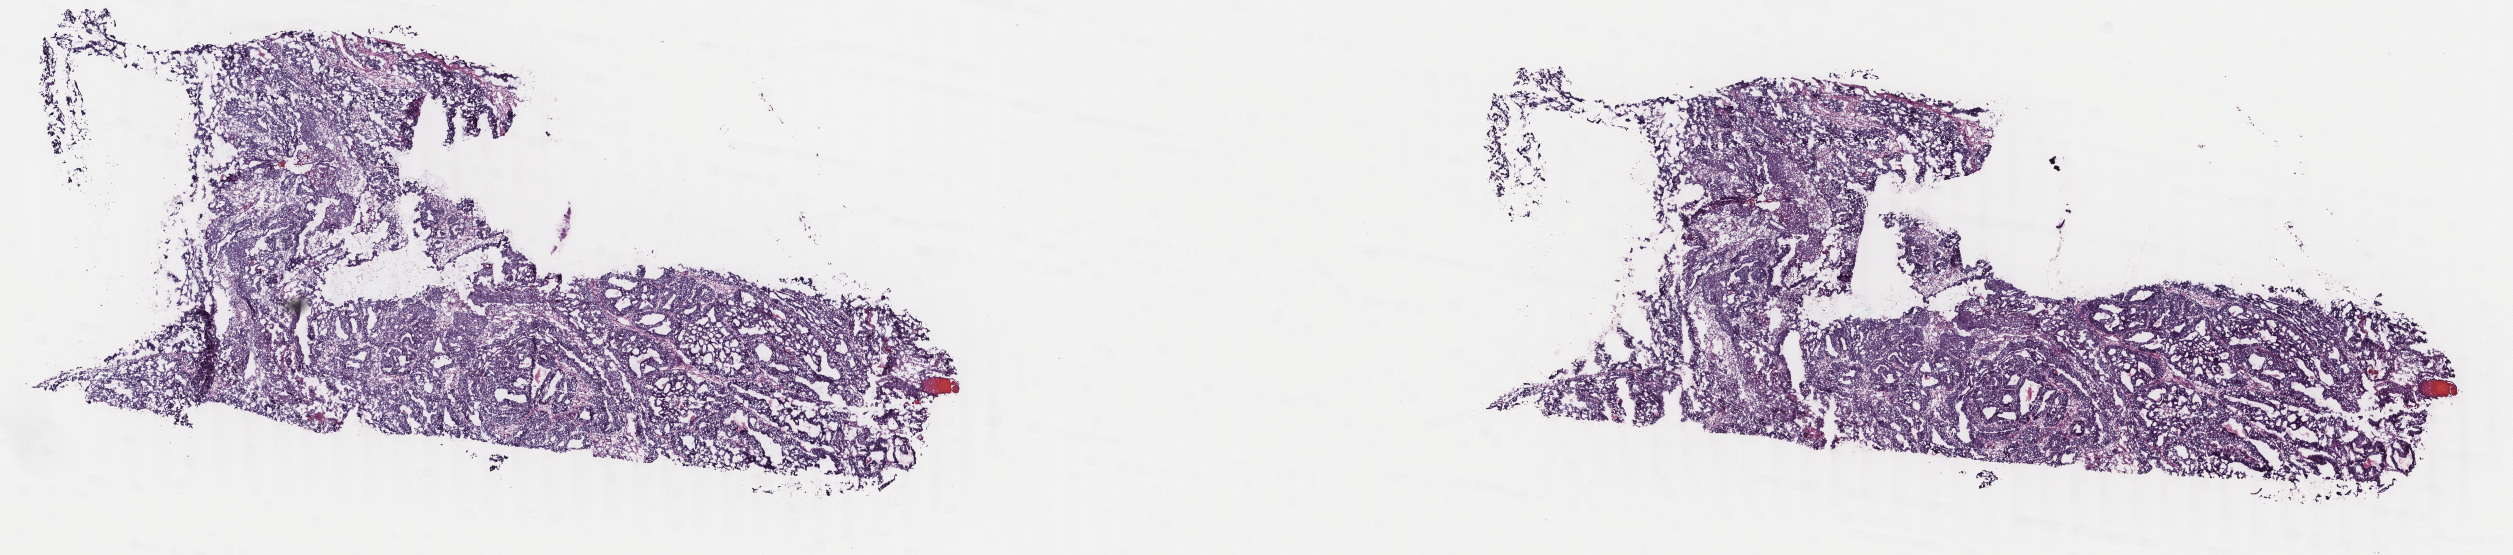
H&E whole-slide image, shown as a low-resolution overview of the whole scanned area (about 20.0 x 4.4 mm, from a 40x scan), frozen section, uterus, primary tumour sample. Patient: female, age at initial diagnosis 55 years. Histologic grade: G2 (moderately differentiated). Composition of this section per pathologist review: tumour cells 100%, tumour nuclei 80%, normal cells 0%, stromal cells 0%, necrosis 0%. Inflammatory infiltration, as recorded: lymphocyte infiltration 0%, monocyte infiltration 0%, neutrophil infiltration 0%.
Diagnosis: Endometrioid adenocarcinoma, NOS. FIGO stage: IA.